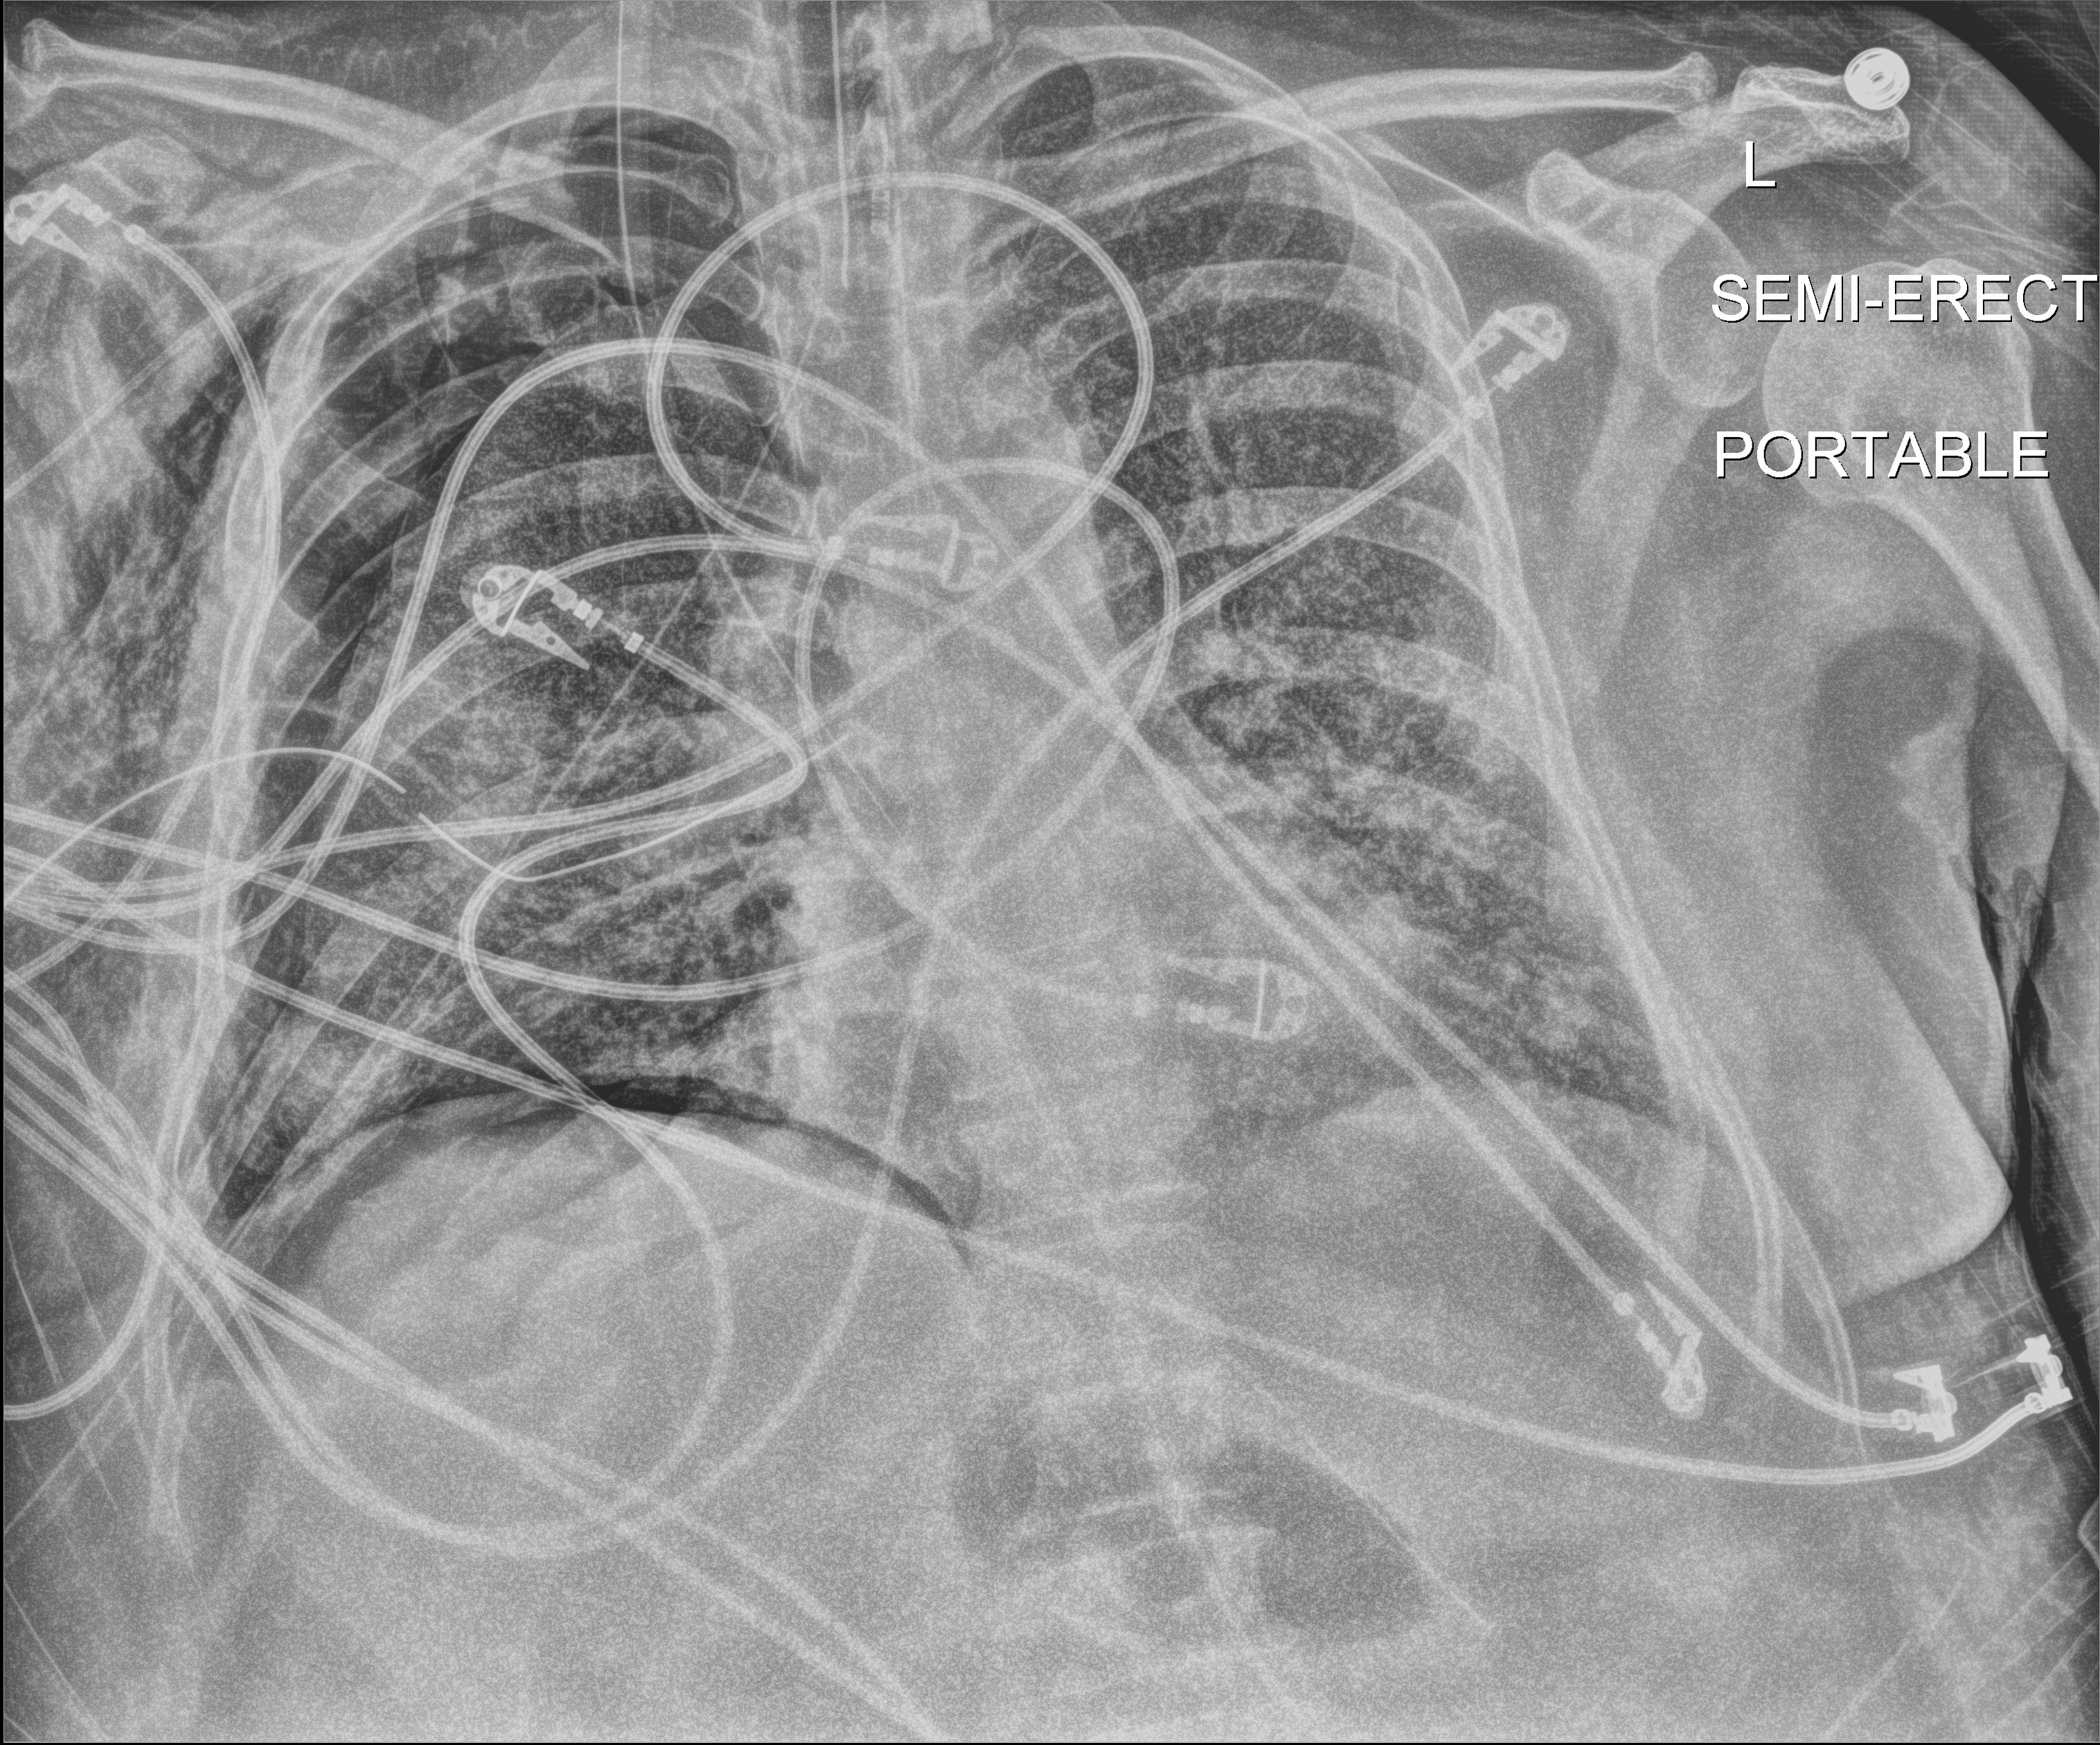
Chest X-ray (portable), anteroposterior (AP) projection. Patient hospitalised with COVID-19, aged 18–59 years.
Hospital-stay facts (about this admission, not read from this image; timing relative to this image not recorded):
- mechanically ventilated during this hospital stay: yes
- admitted to intensive care during this hospital stay: yes